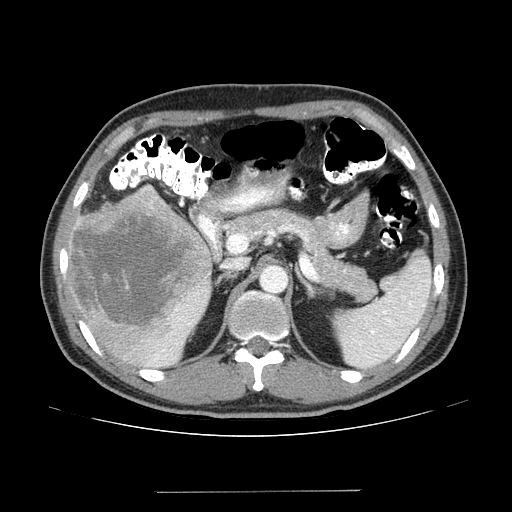
Contrast-enhanced abdominal CT (liver protocol), one axial slice. Slice 79 of 131 in the series (ordered by position). One of 2 acquisitions stored at this slice position. Soft-tissue window (W 400 / L 40 HU). 2.5 mm slice thickness. 512 × 512 image matrix, field of view 380 × 380 mm. From the clinical record (not read from this slice): diagnosis: hepatocellular carcinoma (patient treated with transarterial chemoembolisation; whether this scan precedes or follows treatment is not stated here); TNM stage (as recorded): Stage-I; Child-Pugh class: A.
Structures marked on this image (semi-automatic segmentation, software-assisted and operator-edited):
- liver parenchyma outside the tumour (the mass and vessels are separate outlines, so this box may not span the whole liver): bounding box [x1, y1, x2, y2] px = [64, 186, 212, 366]
- mass: [67, 186, 212, 333]
- liver vessels: [154, 293, 198, 362]